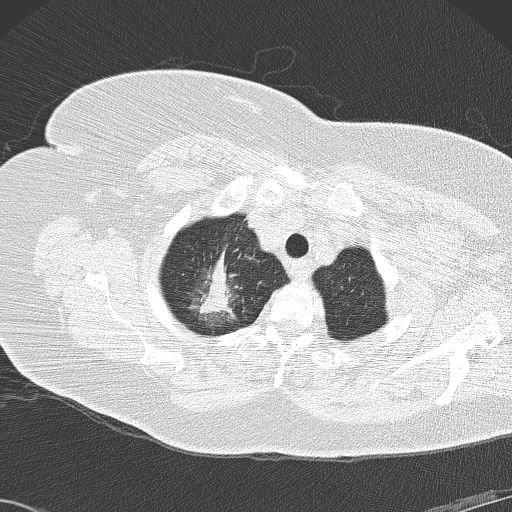
Chest CT (low-dose screening protocol), one axial image, second screening round (one year after baseline), lung window (W 1500 / L -600 HU), 2 mm slice thickness, lung (sharp) reconstruction kernel (B50f), slice 19 of 146 in the series, 512 × 512 image matrix. Female participant, aged 72 years at enrolment. Former smoker at enrolment.
Lesion marked by an expert reader, bounding box <182,245,258,326> (left, top, right, bottom; pixels). The screening reader recorded 4 non-calcified nodules or masses ≥4 mm on this exam; which of them this box marks is not recorded. Official screen result: positive, other. Lung cancer was diagnosed 52 days after this screen: bronchiolo-alveolar adenocarcinoma, NOS, right upper lobe, stage IIIB (AJCC 6th edition), 45 mm at pathology.